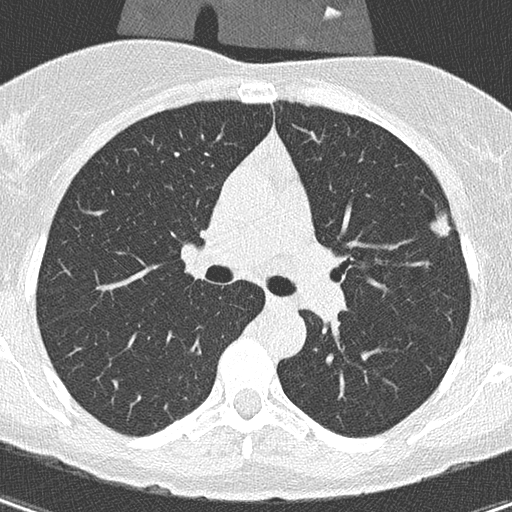
Chest CT (low-dose screening protocol), one axial image; baseline annual screen; lung window (W 1500 / L -600 HU); lung (sharp) reconstruction kernel (B50f); 120 kVp; slice 111 of 305 in the series; 512 × 512 image matrix. Female, age 56 years at enrolment. Former smoker at enrolment.
• Lesion marked by an expert reader, bounding box <421,193,468,247> (left, top, right, bottom; pixels).
• Screening reader's record for this exam (one nodule recorded; not confirmed to be the boxed lesion): non-calcified nodule or mass ≥4 mm, left upper lobe, 110 × 106 mm, spiculated (stellate) margins, soft tissue attenuation.
• Lung cancer was diagnosed 417 days after this screen (after the second annual screen): adenocarcinoma, NOS, left upper lobe, moderately differentiated (G2), stage IA (AJCC 6th edition), 11 mm at pathology.